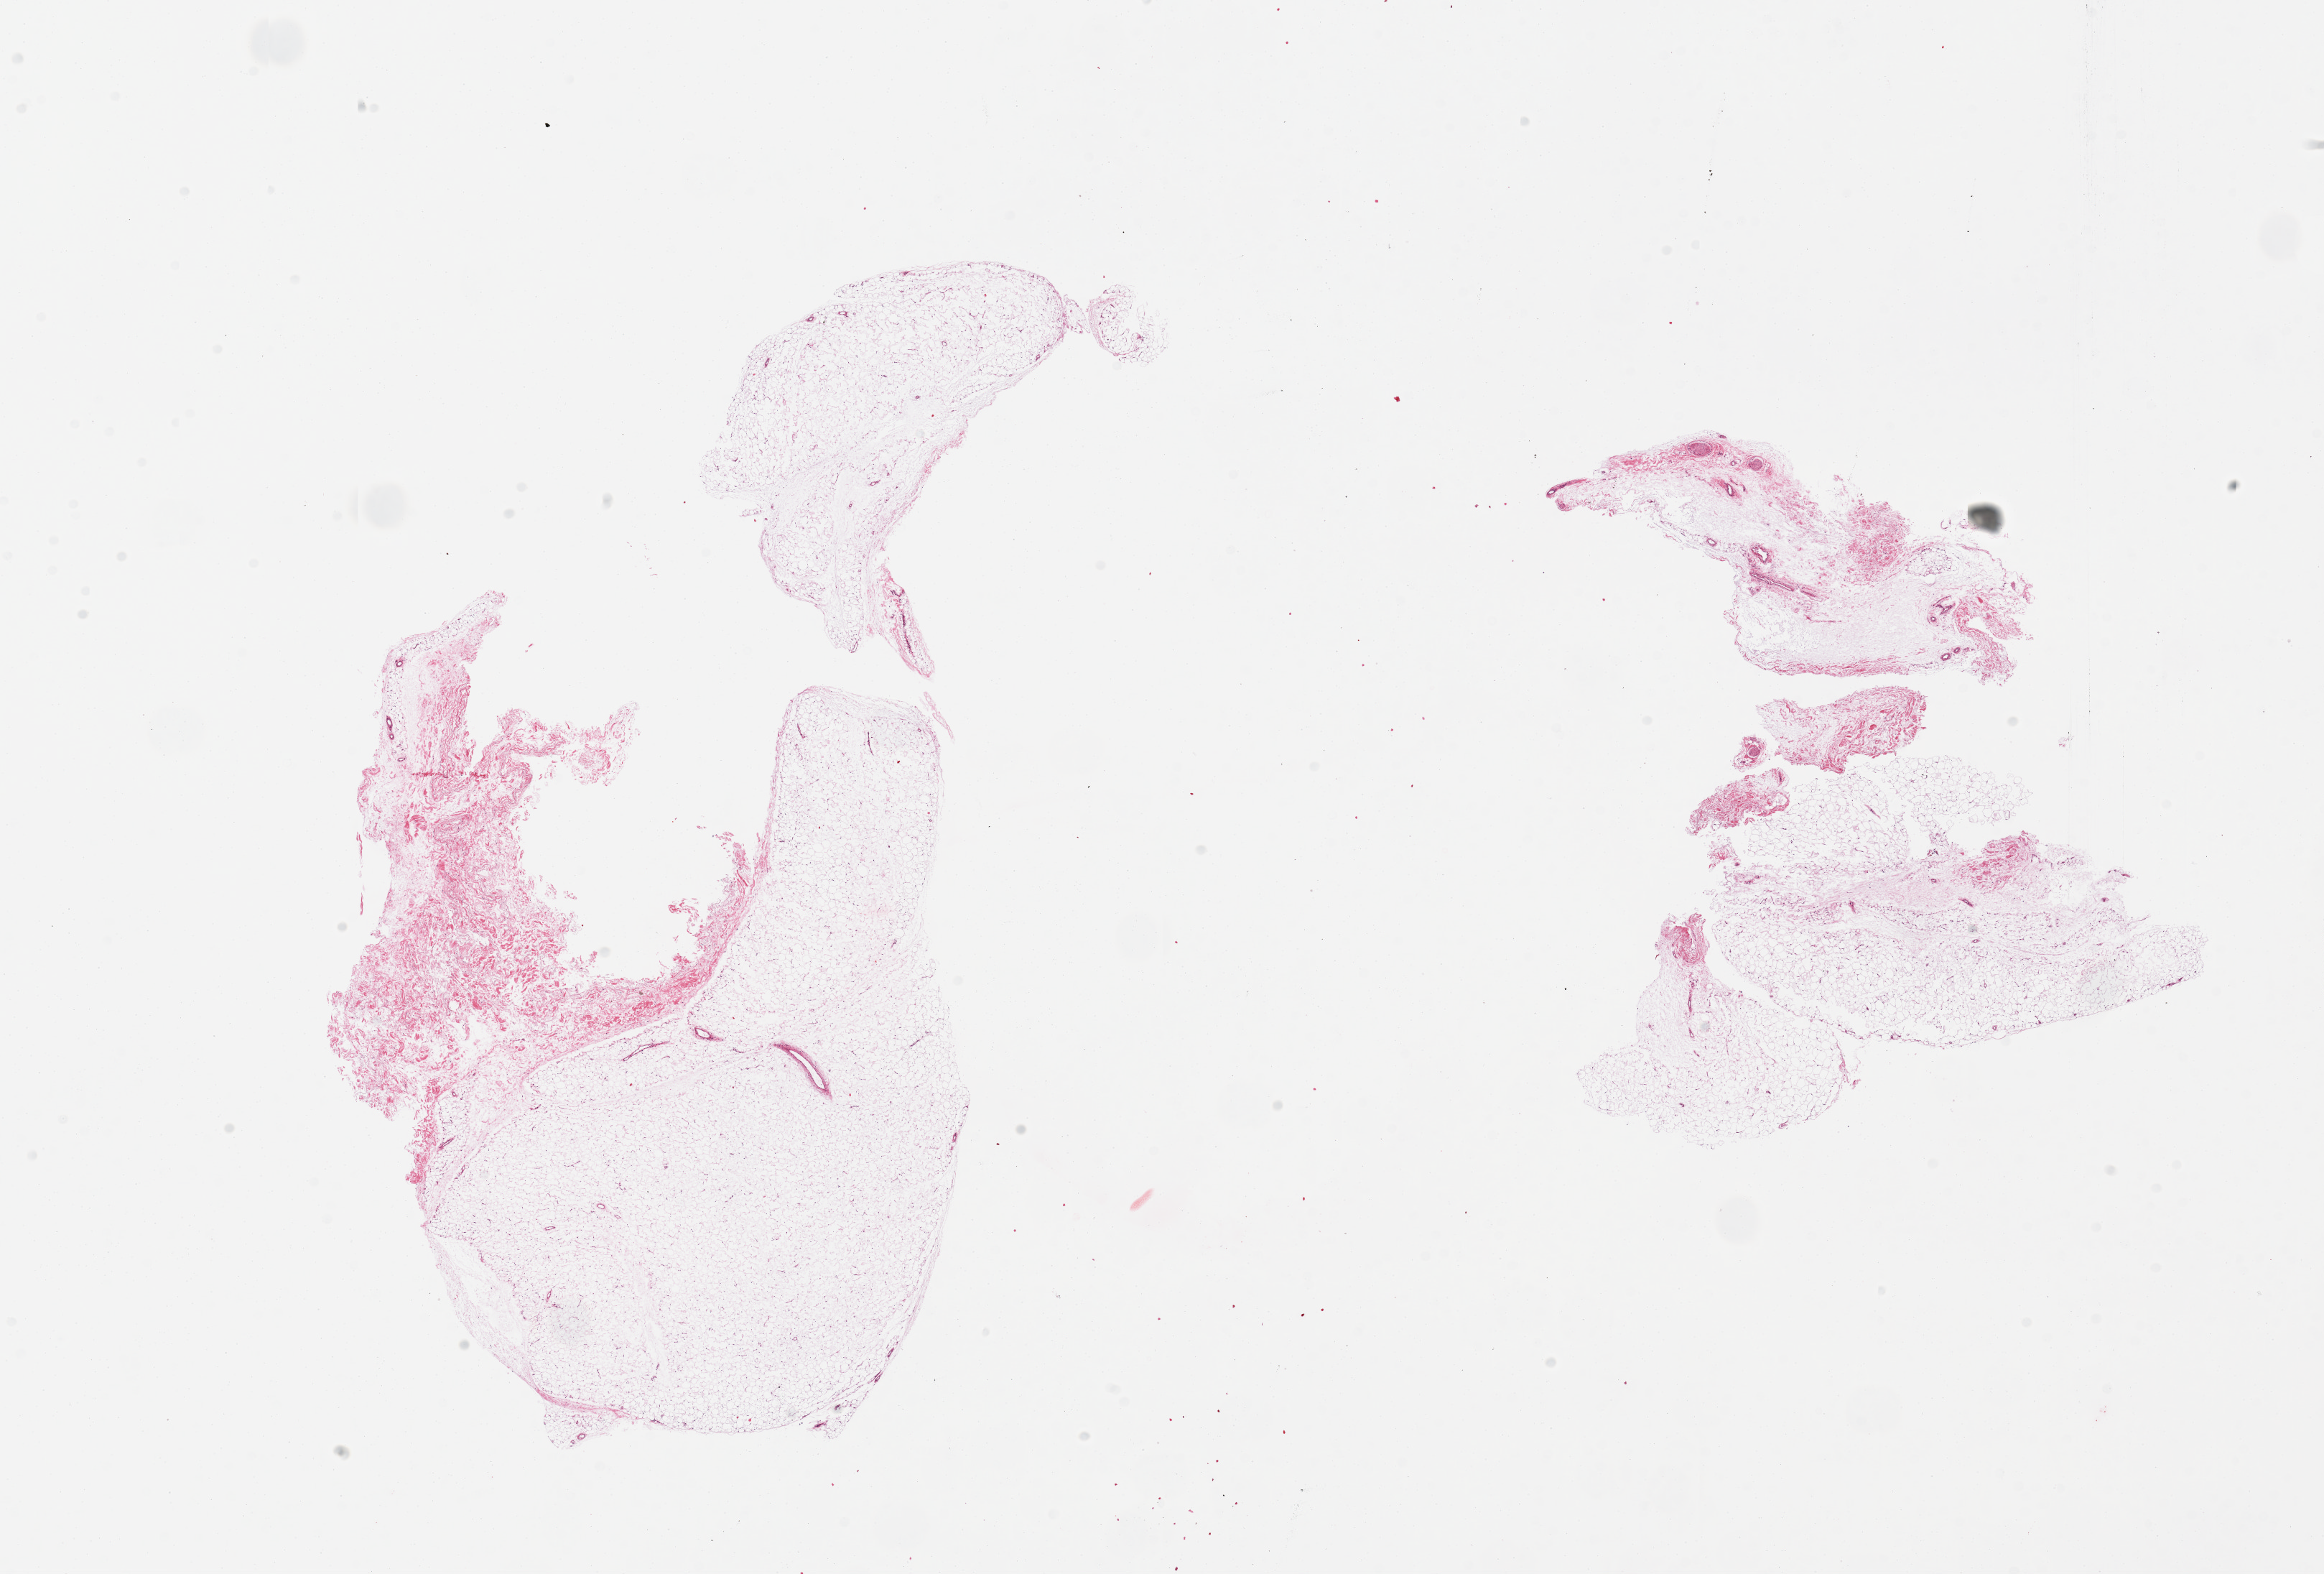
Haematoxylin and eosin whole-slide image — shown as a low-resolution overview of the whole scanned area (about 25.6 x 17.3 mm); PAXgene-fixed, paraffin-embedded tissue; section of adipose tissue (target tissue); donor tissue sample. Donor sex: male.
- reviewer comment on this tissue sample: 2 pieces